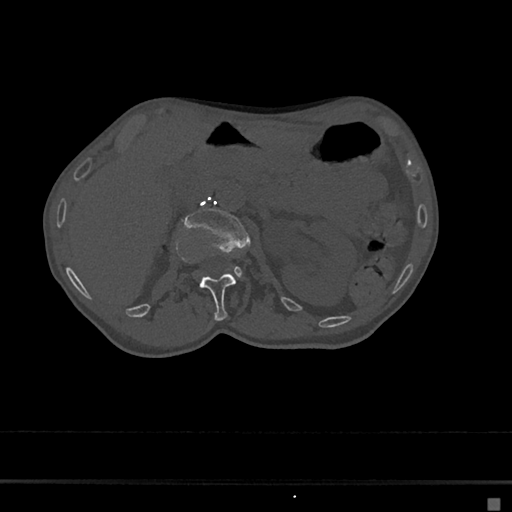
CT including the spine, one axial slice; position 54 of 797 along the scan axis; 120 kVp; bone window (W 1800 / L 400 HU); 512 × 512 image matrix, field of view 360 × 360 mm. Female patient, age 68 years. From the clinical record (not read from this slice): primary cancer: renal.
Outlined on this slice (semi-automatically segmented with operator editing):
- L1 vertebra: box from (x=191, y=258) to (x=236, y=321) px
- L2 vertebra: (x=185, y=207)–(x=248, y=275)